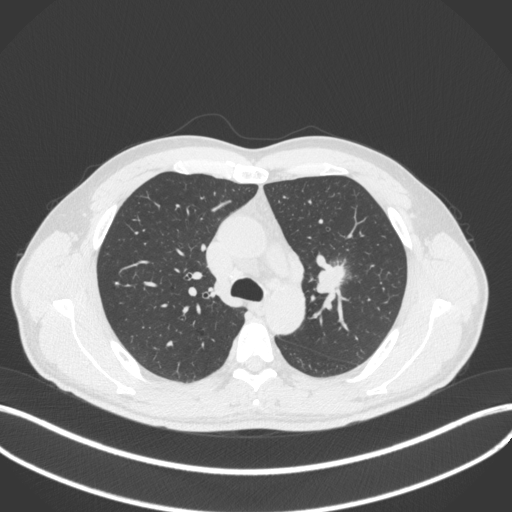
Chest CT, one axial slice; position 289 of 383 along the scan axis; lung window (W 1500 / L -600 HU); 1 mm slice thickness; 512 × 512 image matrix, field of view 400 × 400 mm. Patient: male, 50 years. From the clinical record (not read from this slice): clinical TNM (as recorded): T1c N1 M1b.
Annotated regions visible in this slice (rectangle marked by the reading radiologist):
- lung tumour (recorded histology: squamous cell carcinoma): bounding box (x1, y1, x2, y2) in pixels: (315, 255, 347, 298)